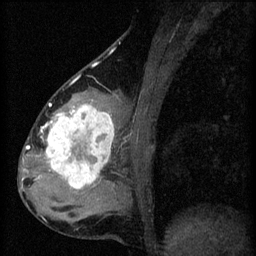
Breast MRI (dynamic contrast-enhanced), one sagittal slice; position 25 of 60 along the scan axis; 3 images stored at this slice position (order not interpretable as contrast timing); 1.5 T; TE 4.2 ms, TR 8.2 ms; 2 mm slice thickness; 256 × 256 image matrix, field of view 180 × 180 mm. Patient: female, 37 years.
Structures marked on this image (semi-automatic segmentation, software-assisted and operator-edited):
- analysis volume of interest (the breast-tissue region the enhancement analysis was run in; not a lesion): box from (x=44, y=100) to (x=119, y=197) px
- tumour enhancement mask (voxels above the 70 % enhancement threshold inside the analysis volume of interest): (x=44, y=104)–(x=115, y=189)